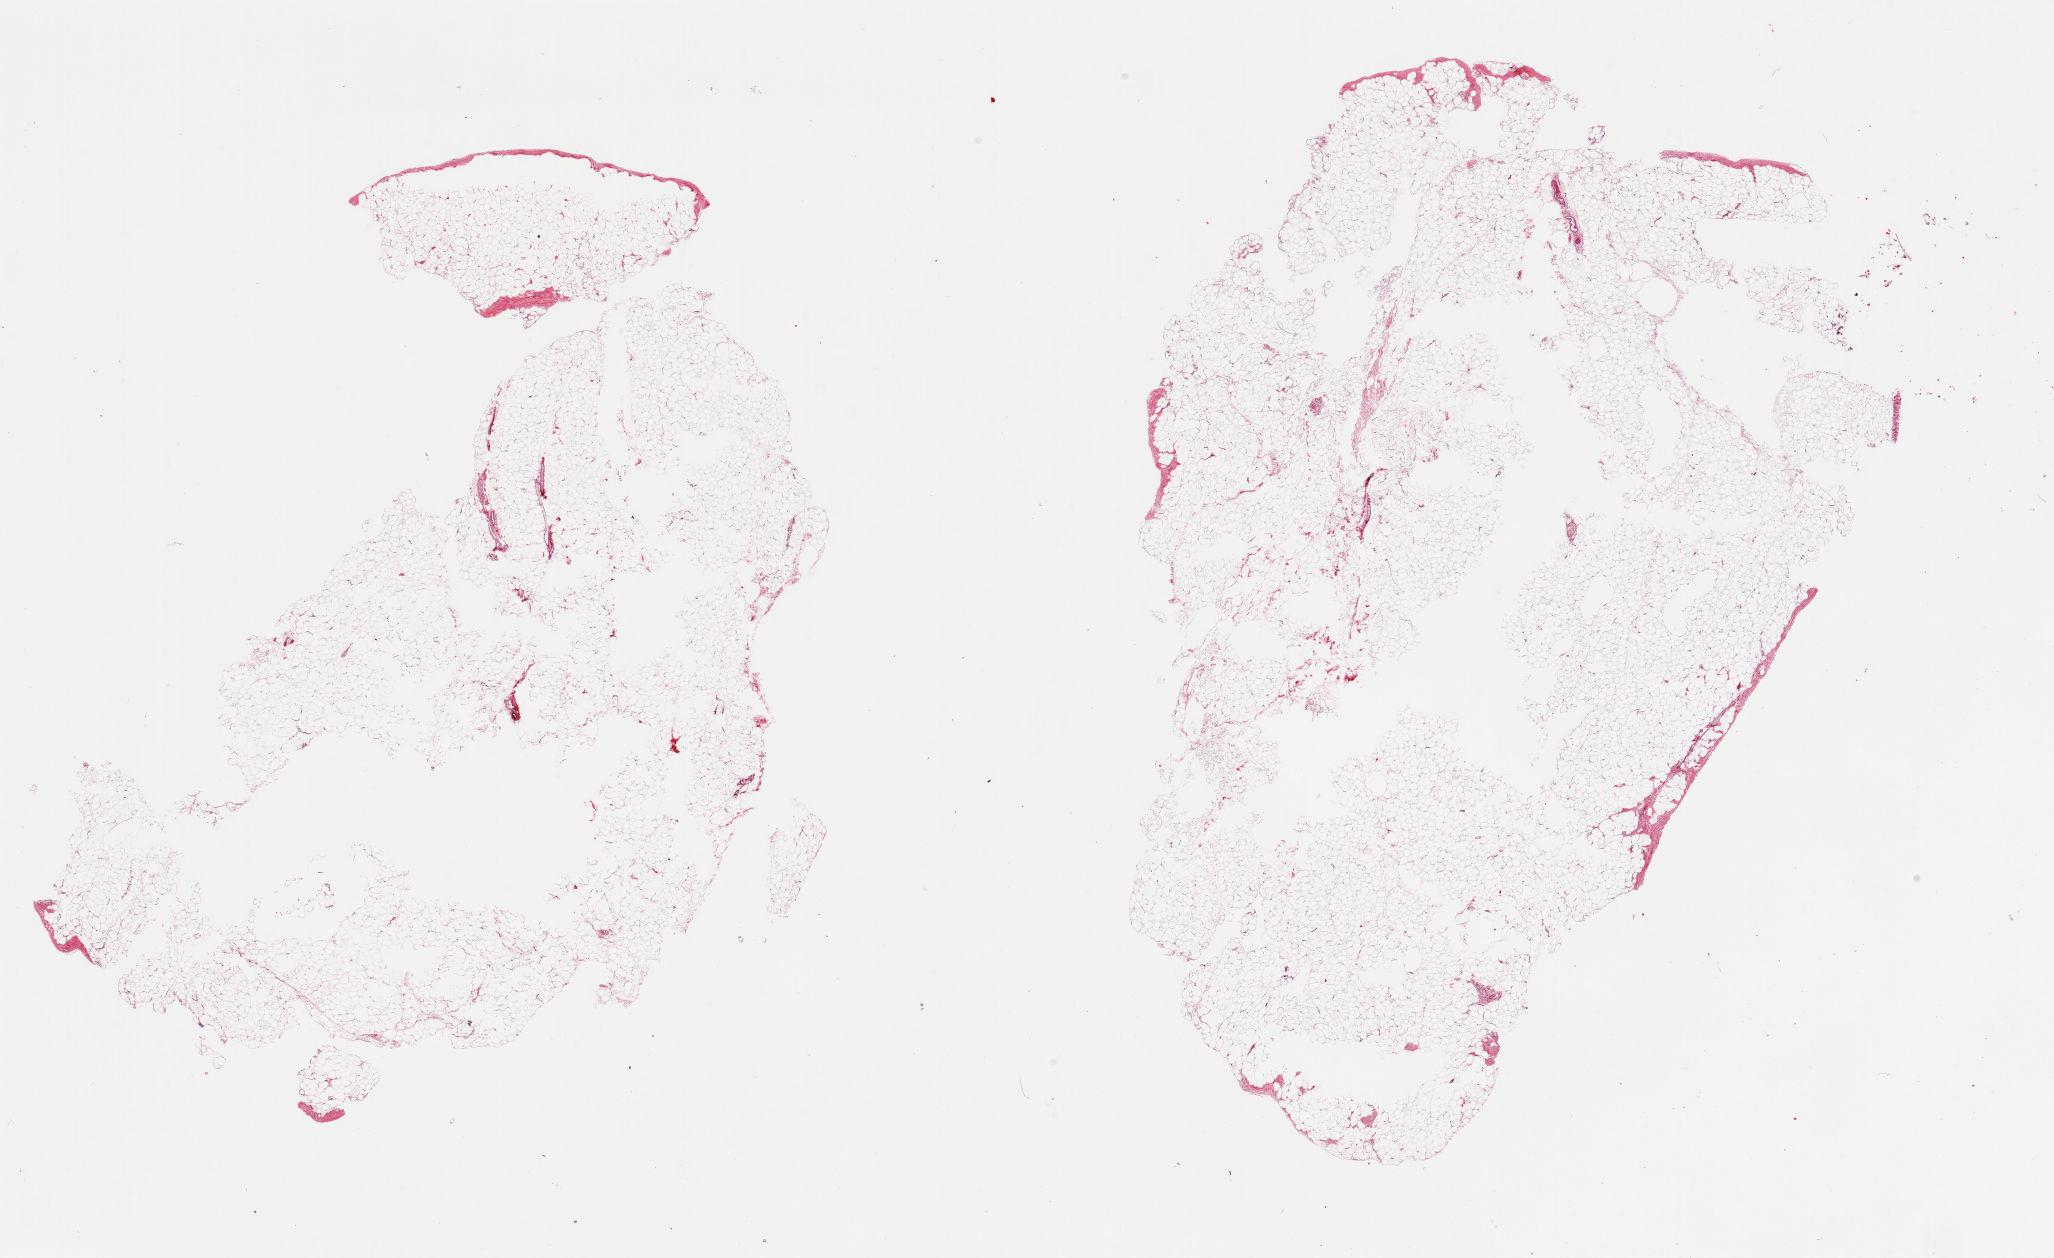
Whole-slide image, haematoxylin and eosin stain — shown as a low-resolution overview of the whole scanned area (about 32.5 x 19.9 mm), PAXgene-fixed paraffin-embedded (PFPE) section, section of omentum (target tissue), donor tissue sample.
Review note (as recorded): 2 pieces. Large specimens with central holes.